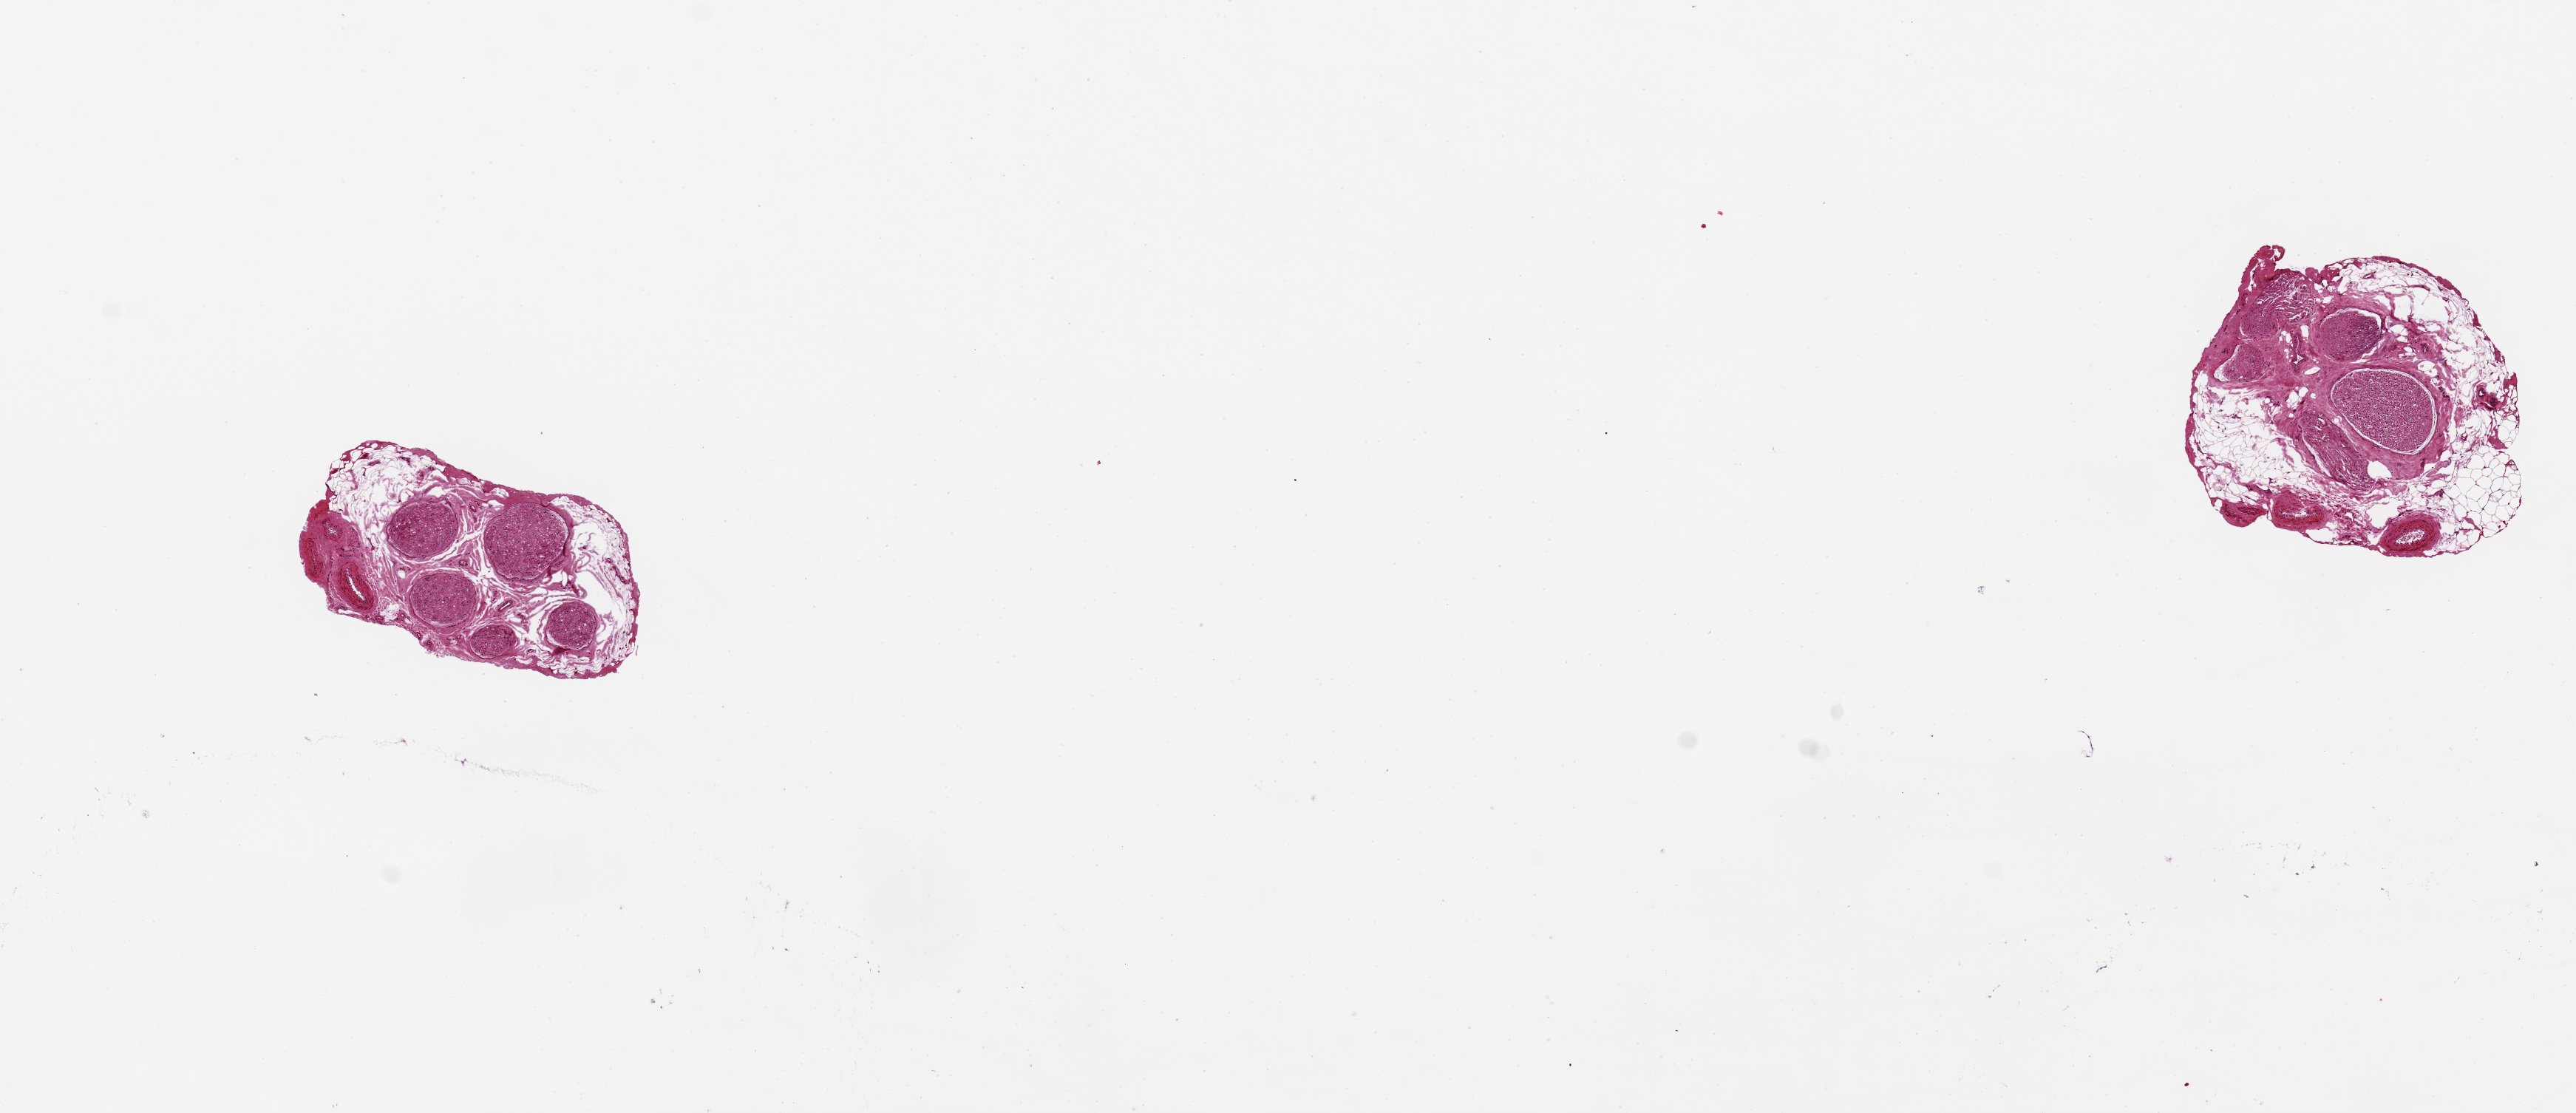
Hematoxylin and eosin (H&E) whole-slide image, brightfield, low-resolution overview of the scanned area, about 13.8 x 6.0 mm; PAXgene-fixed paraffin-embedded (PFPE) section; section of tibial nerve (target tissue); tissue donor sample. Donor: female.
• reviewer comment on this tissue sample: 2 pieces, ~1.8x1mm, ~50% fat and blood vessels